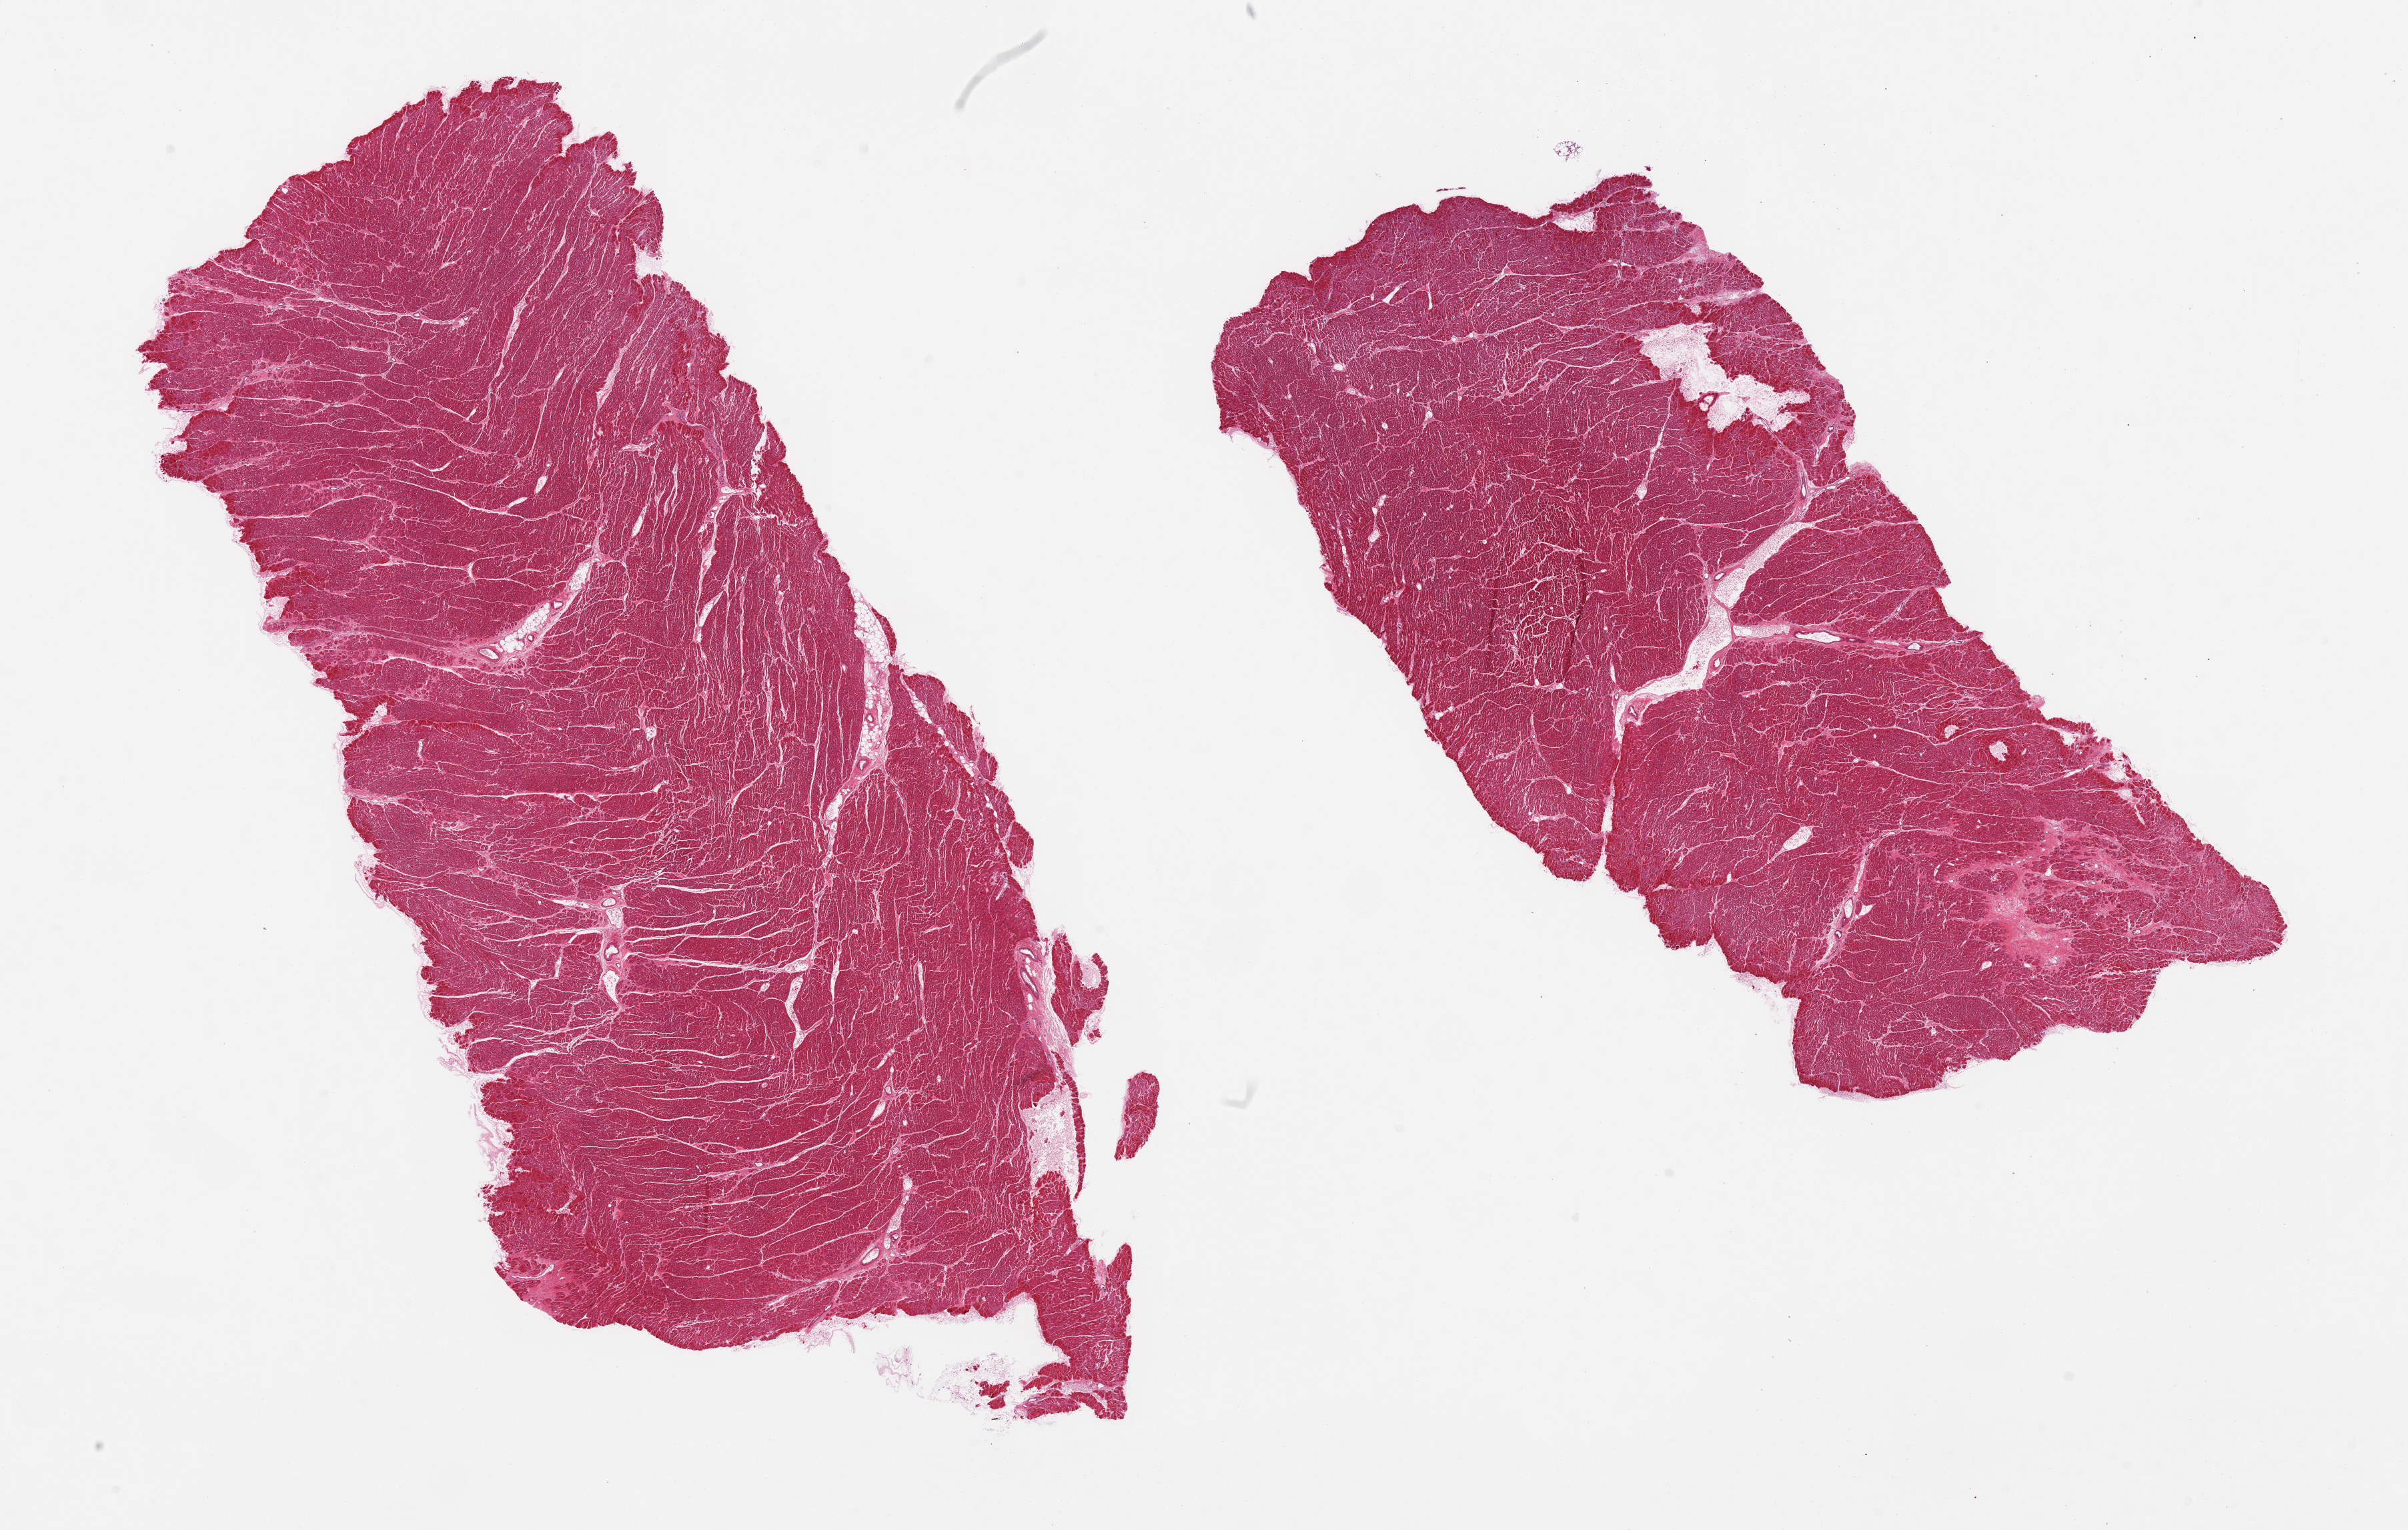
Haematoxylin and eosin whole-slide image — whole scanned area (about 28.5 x 18.1 mm) shown as a low-resolution overview; PAXgene-fixed paraffin-embedded (PFPE) section; sampled site (target tissue): heart; donor tissue sample. Donor sex: male.
Review note (as recorded): 2 pieces; scarred area 1.5x1.5mm (old infarct); hypertensive nuclear changes.